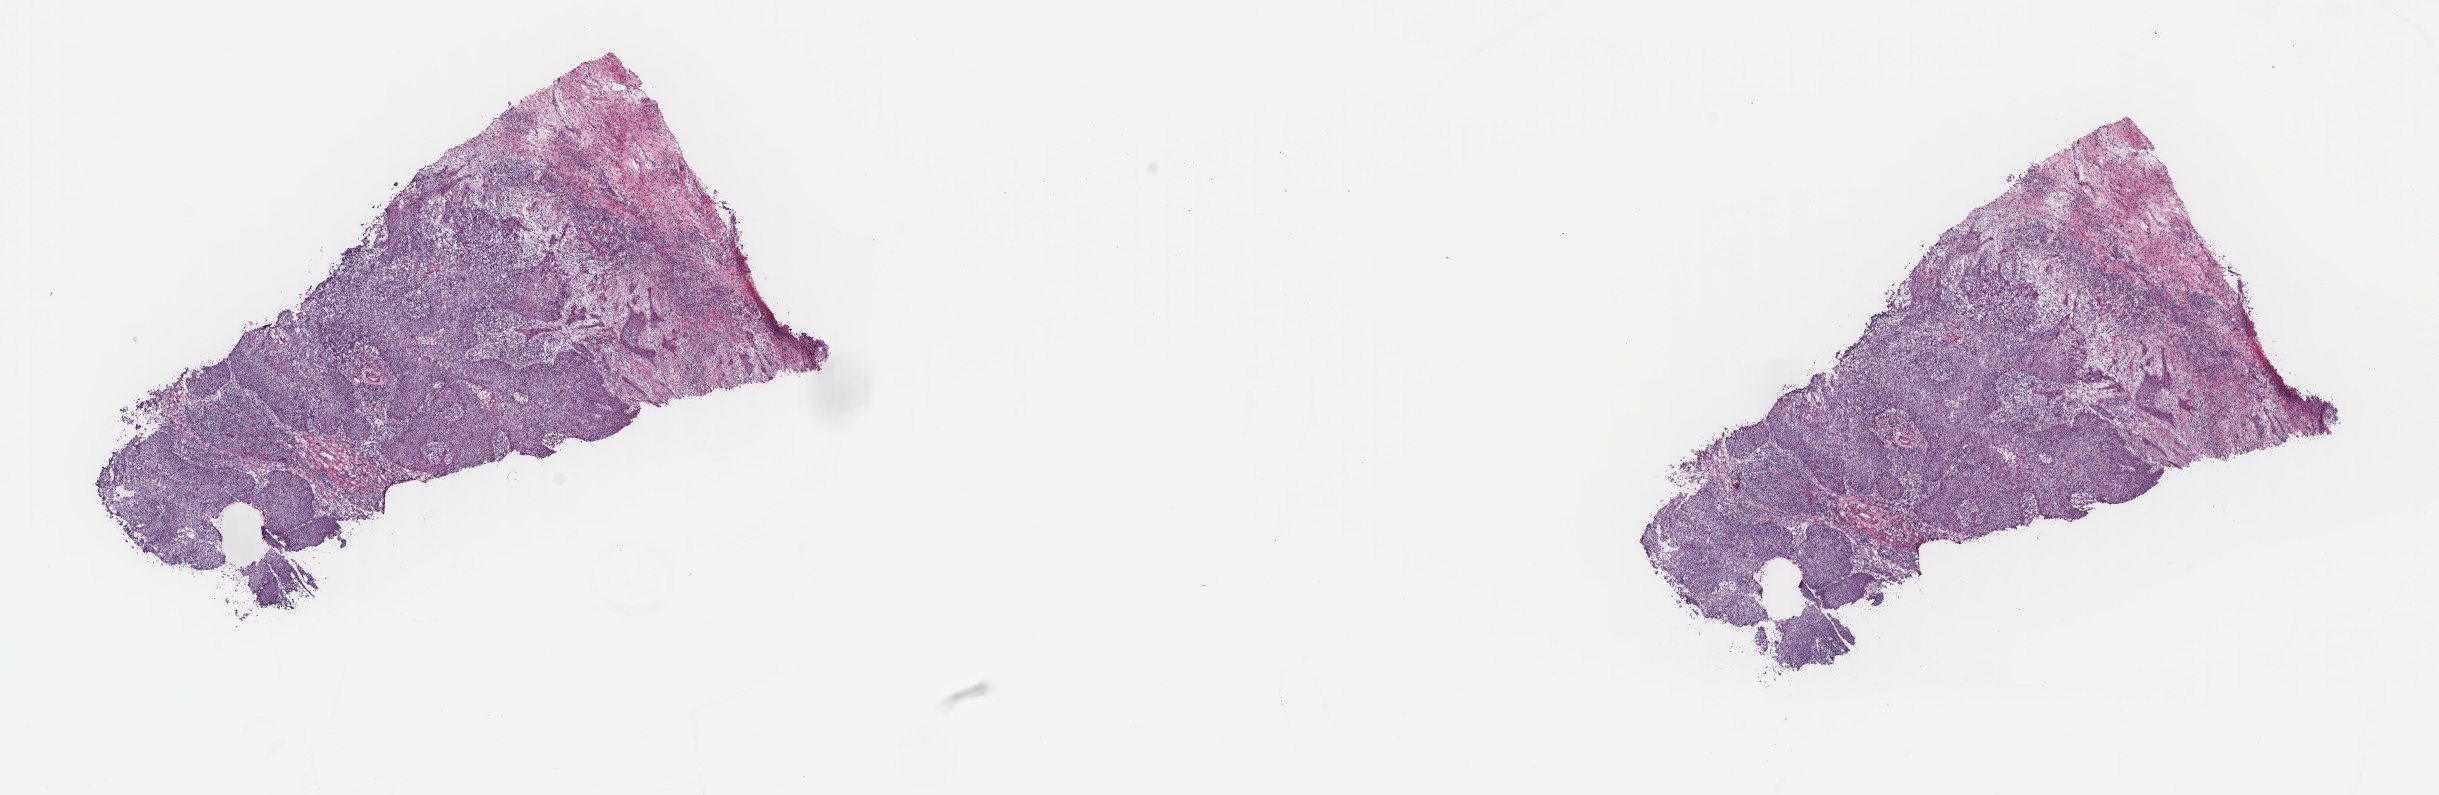
H&E whole-slide image — whole scanned area (about 19.4 x 6.3 mm) shown as a low-resolution overview; frozen section from the top of the tissue portion; cervix, primary tumour sample. Female patient; age at initial diagnosis 55 years. Histologic grade: G2 (moderately differentiated). Slide review estimates, as recorded: tumour cells 60%, tumour nuclei 60%, normal cells 0%, stromal cells 35%, necrosis 5%. Infiltration values recorded for this section: lymphocyte infiltration 60%, monocyte infiltration 5%, neutrophil infiltration 20%.
- histologic diagnosis: Squamous cell carcinoma, NOS (cervix uteri)
- FIGO stage: IIIB